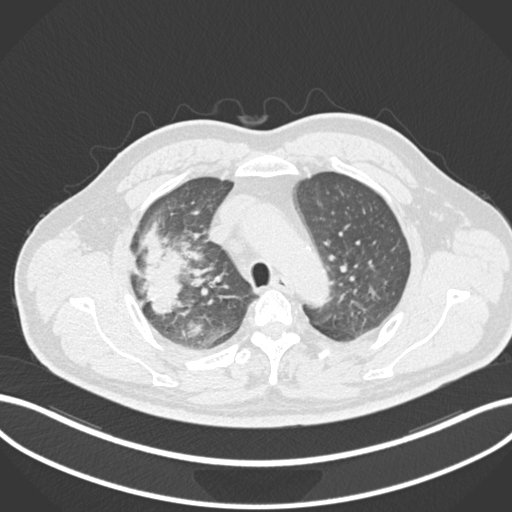
Chest CT, one axial slice; slice 675 of 852 in the series (ordered by position); reconstruction kernel B30f; lung window (W 1500 / L -600 HU); 1 mm slice thickness; 512 × 512 image matrix, field of view 400 × 400 mm. Male patient, age 55 years. Case-level facts recorded for this patient, not image findings: clinical TNM (as recorded): T3 N2 M1.
Outlined on this slice (bounding box drawn by a radiologist):
- lung tumour (recorded histology: adenocarcinoma): bounding box <138,222,189,315> (left, top, right, bottom; pixels)